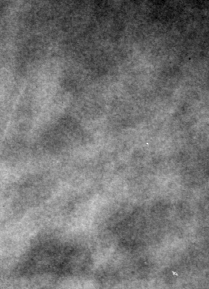
Cropped region of a digitized screen-film mammogram centred on a radiologist-marked abnormality; right breast; MLO view.
Marked abnormality: calcifications, morphology punctate / round and regular, distribution regional; BI-RADS assessment category 2; subtlety rating 3 on a 1 (subtle) to 5 (obvious) scale; benign without callback (not worked up further).